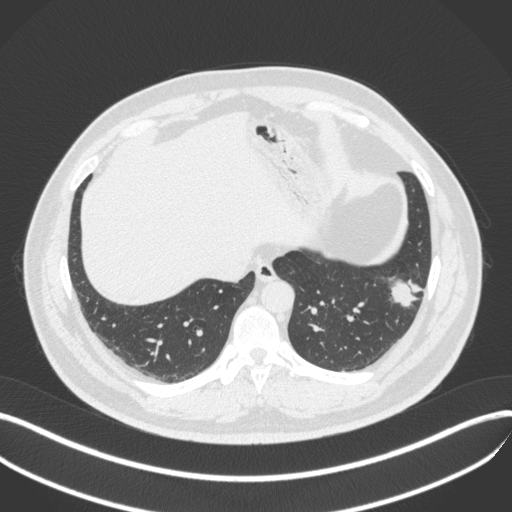
Chest CT, one axial slice; position 114 of 420 along the scan axis; reconstruction kernel B31f; lung window (W 1500 / L -600 HU); 1 mm slice thickness; 512 × 512 image matrix. Patient: male, 39 years. Case-level facts recorded for this patient, not image findings: clinical TNM (as recorded): T2a N0 M0; histopathological grade: G2-3.
Outlined on this slice (bounding box drawn by a radiologist):
- lung tumour (recorded histology: adenocarcinoma): box from (x=385, y=268) to (x=425, y=311) px